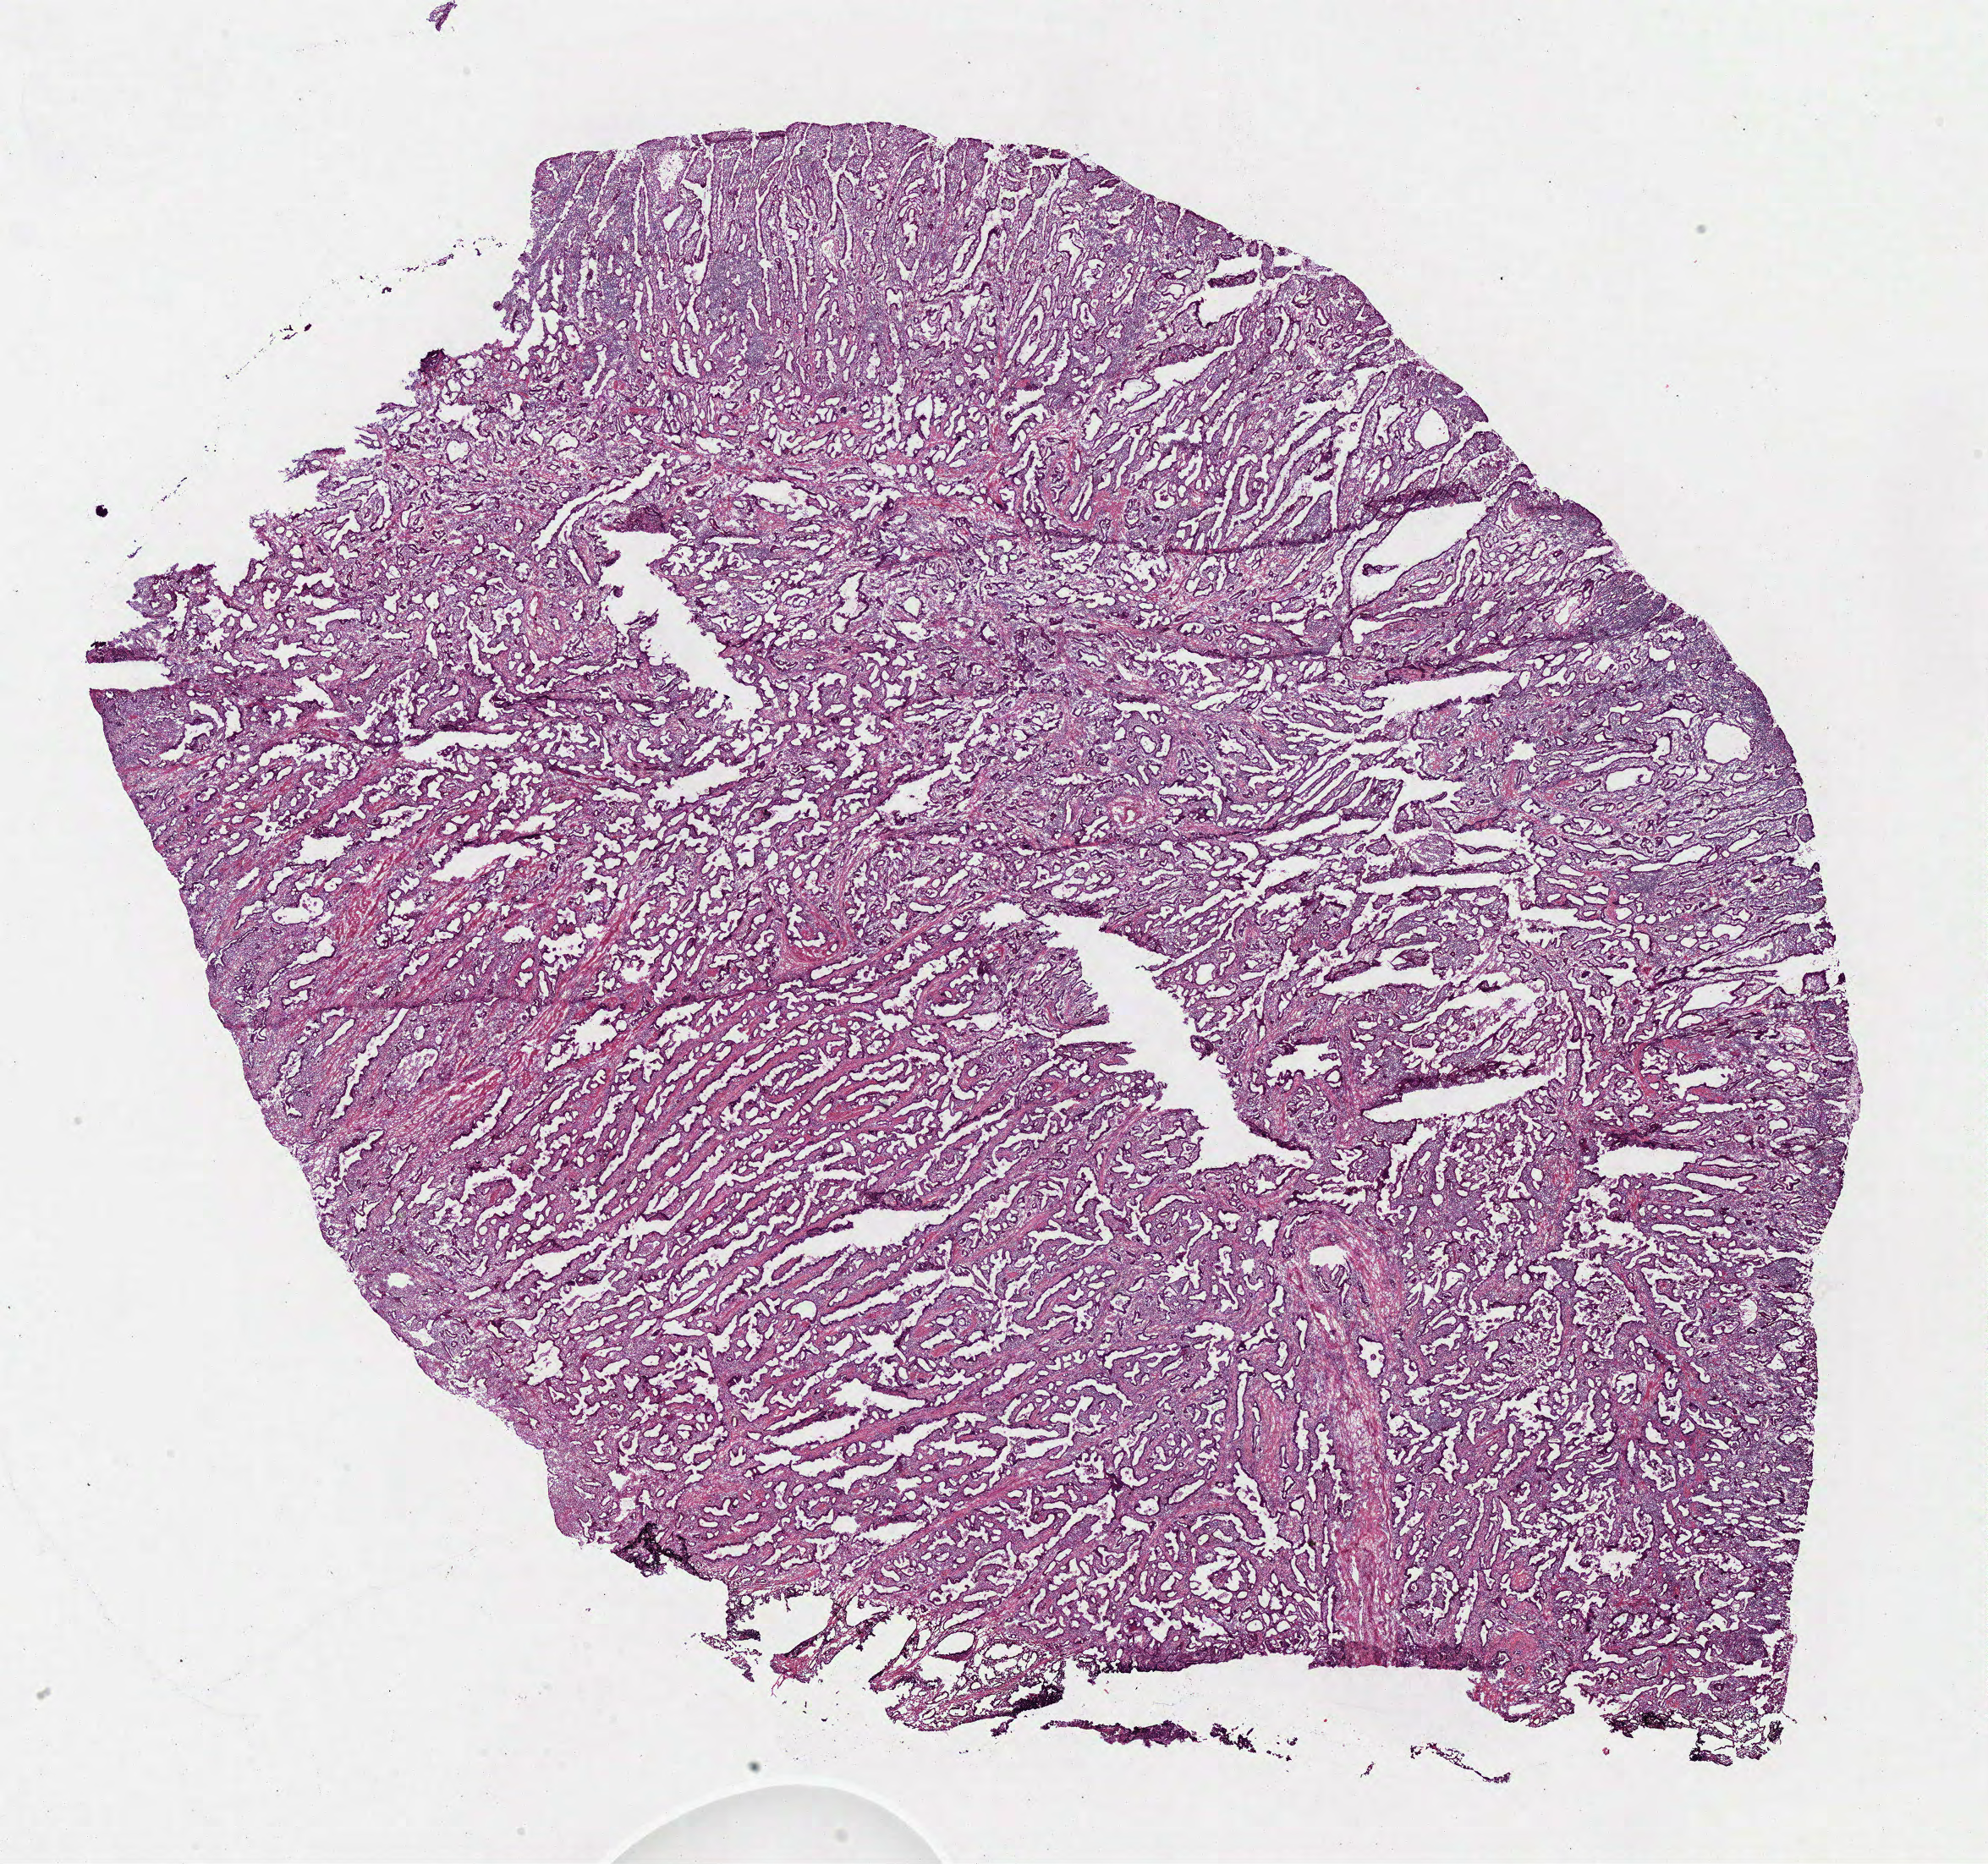
Hematoxylin and eosin (H&E) stained whole-slide image, a low-resolution overview of the entire scanned area, about 18.5 x 17.4 mm, frozen section from the bottom of the tissue portion, sample: primary tumour, stomach. Male patient; age at initial diagnosis 58 years. Histologic grade: G3 (poorly differentiated). Pathologist review of this section (percent, as recorded): tumour cells 100%, tumour nuclei 55%, normal cells 0%, stromal cells 0%, necrosis 0%. Infiltration values recorded for this section: lymphocyte infiltration 30%, monocyte infiltration 0%, neutrophil infiltration 5%.
- pathologic diagnosis: Adenocarcinoma, NOS (cardia, NOS)
- lymph nodes positive (case pathology): 0 of 5 examined
- AJCC pathologic stage: IIA
- TNM: T3 N0 M0